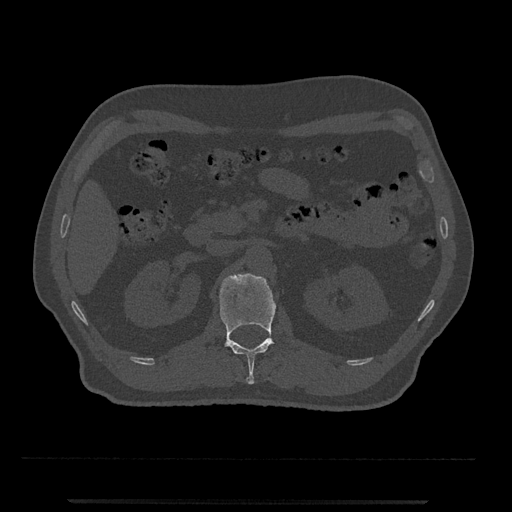
CT including the spine, one axial slice; position 327 of 797 along the scan axis; 120 kVp; bone window (W 1800 / L 400 HU); 0.5 mm slice thickness; 512 × 512 image matrix. Male patient, age 63 years. From the clinical record (not read from this slice): primary cancer: prostate.
Outlined on this slice (semi-automatically segmented with operator editing):
- L1 vertebra: bounding box <220,273,276,384> (left, top, right, bottom; pixels)